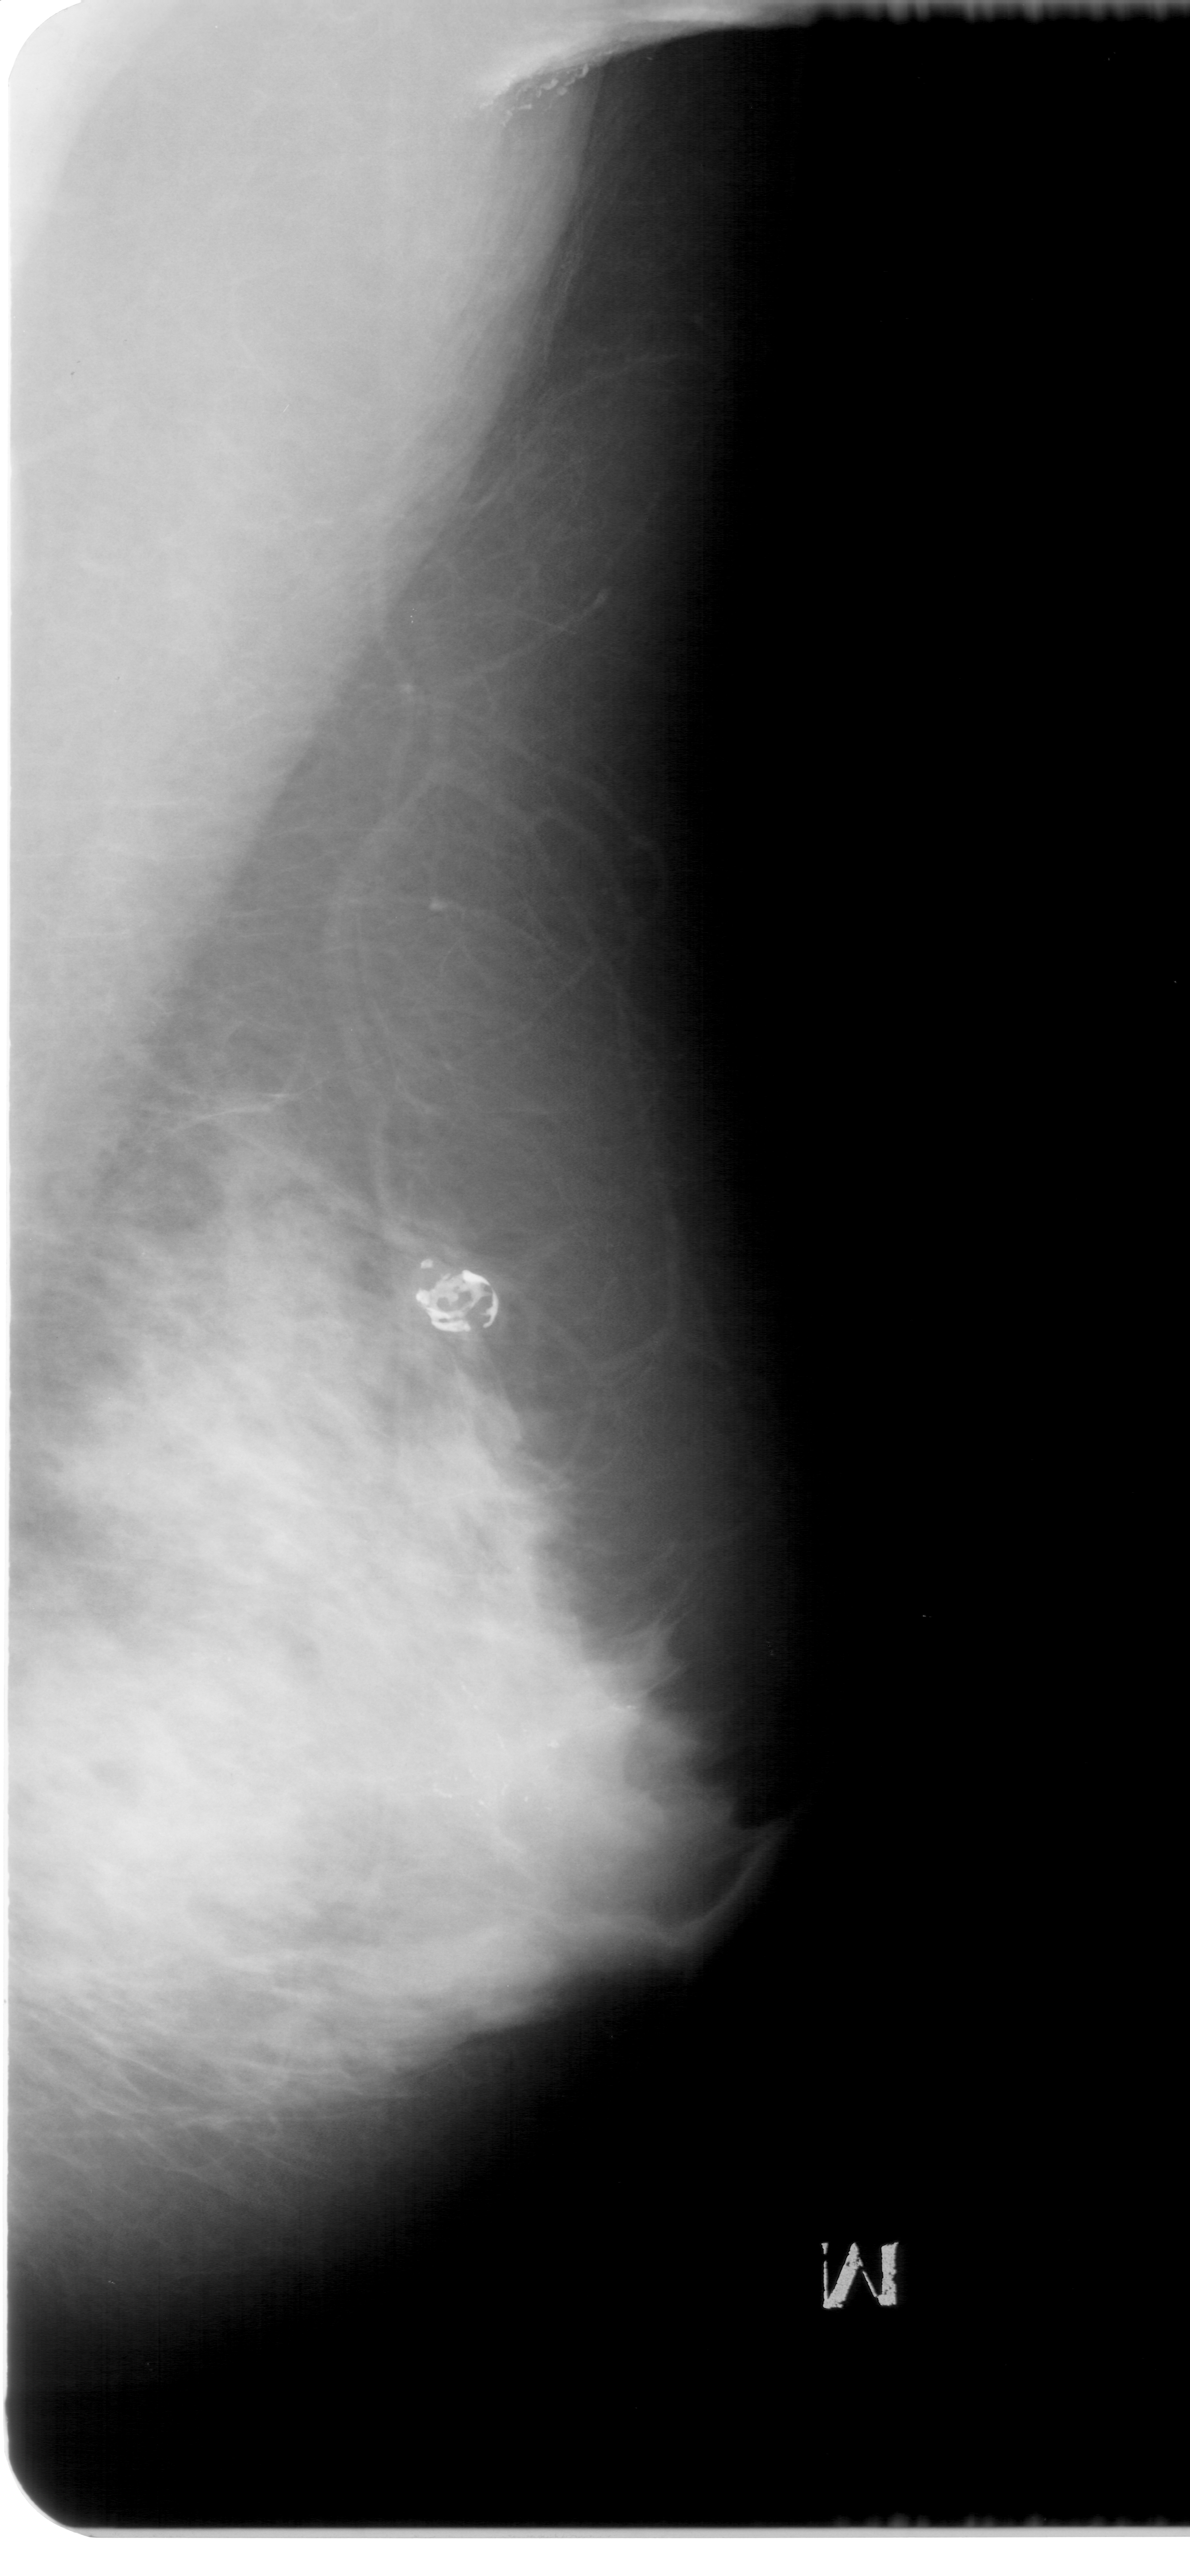
Scanned film-screen mammogram, right breast, MLO view.
Calcifications, morphology pleomorphic, distribution segmental; BI-RADS assessment category 5; subtlety rating 4 on a 1 (subtle) to 5 (obvious) scale; pathology (as recorded): malignant.